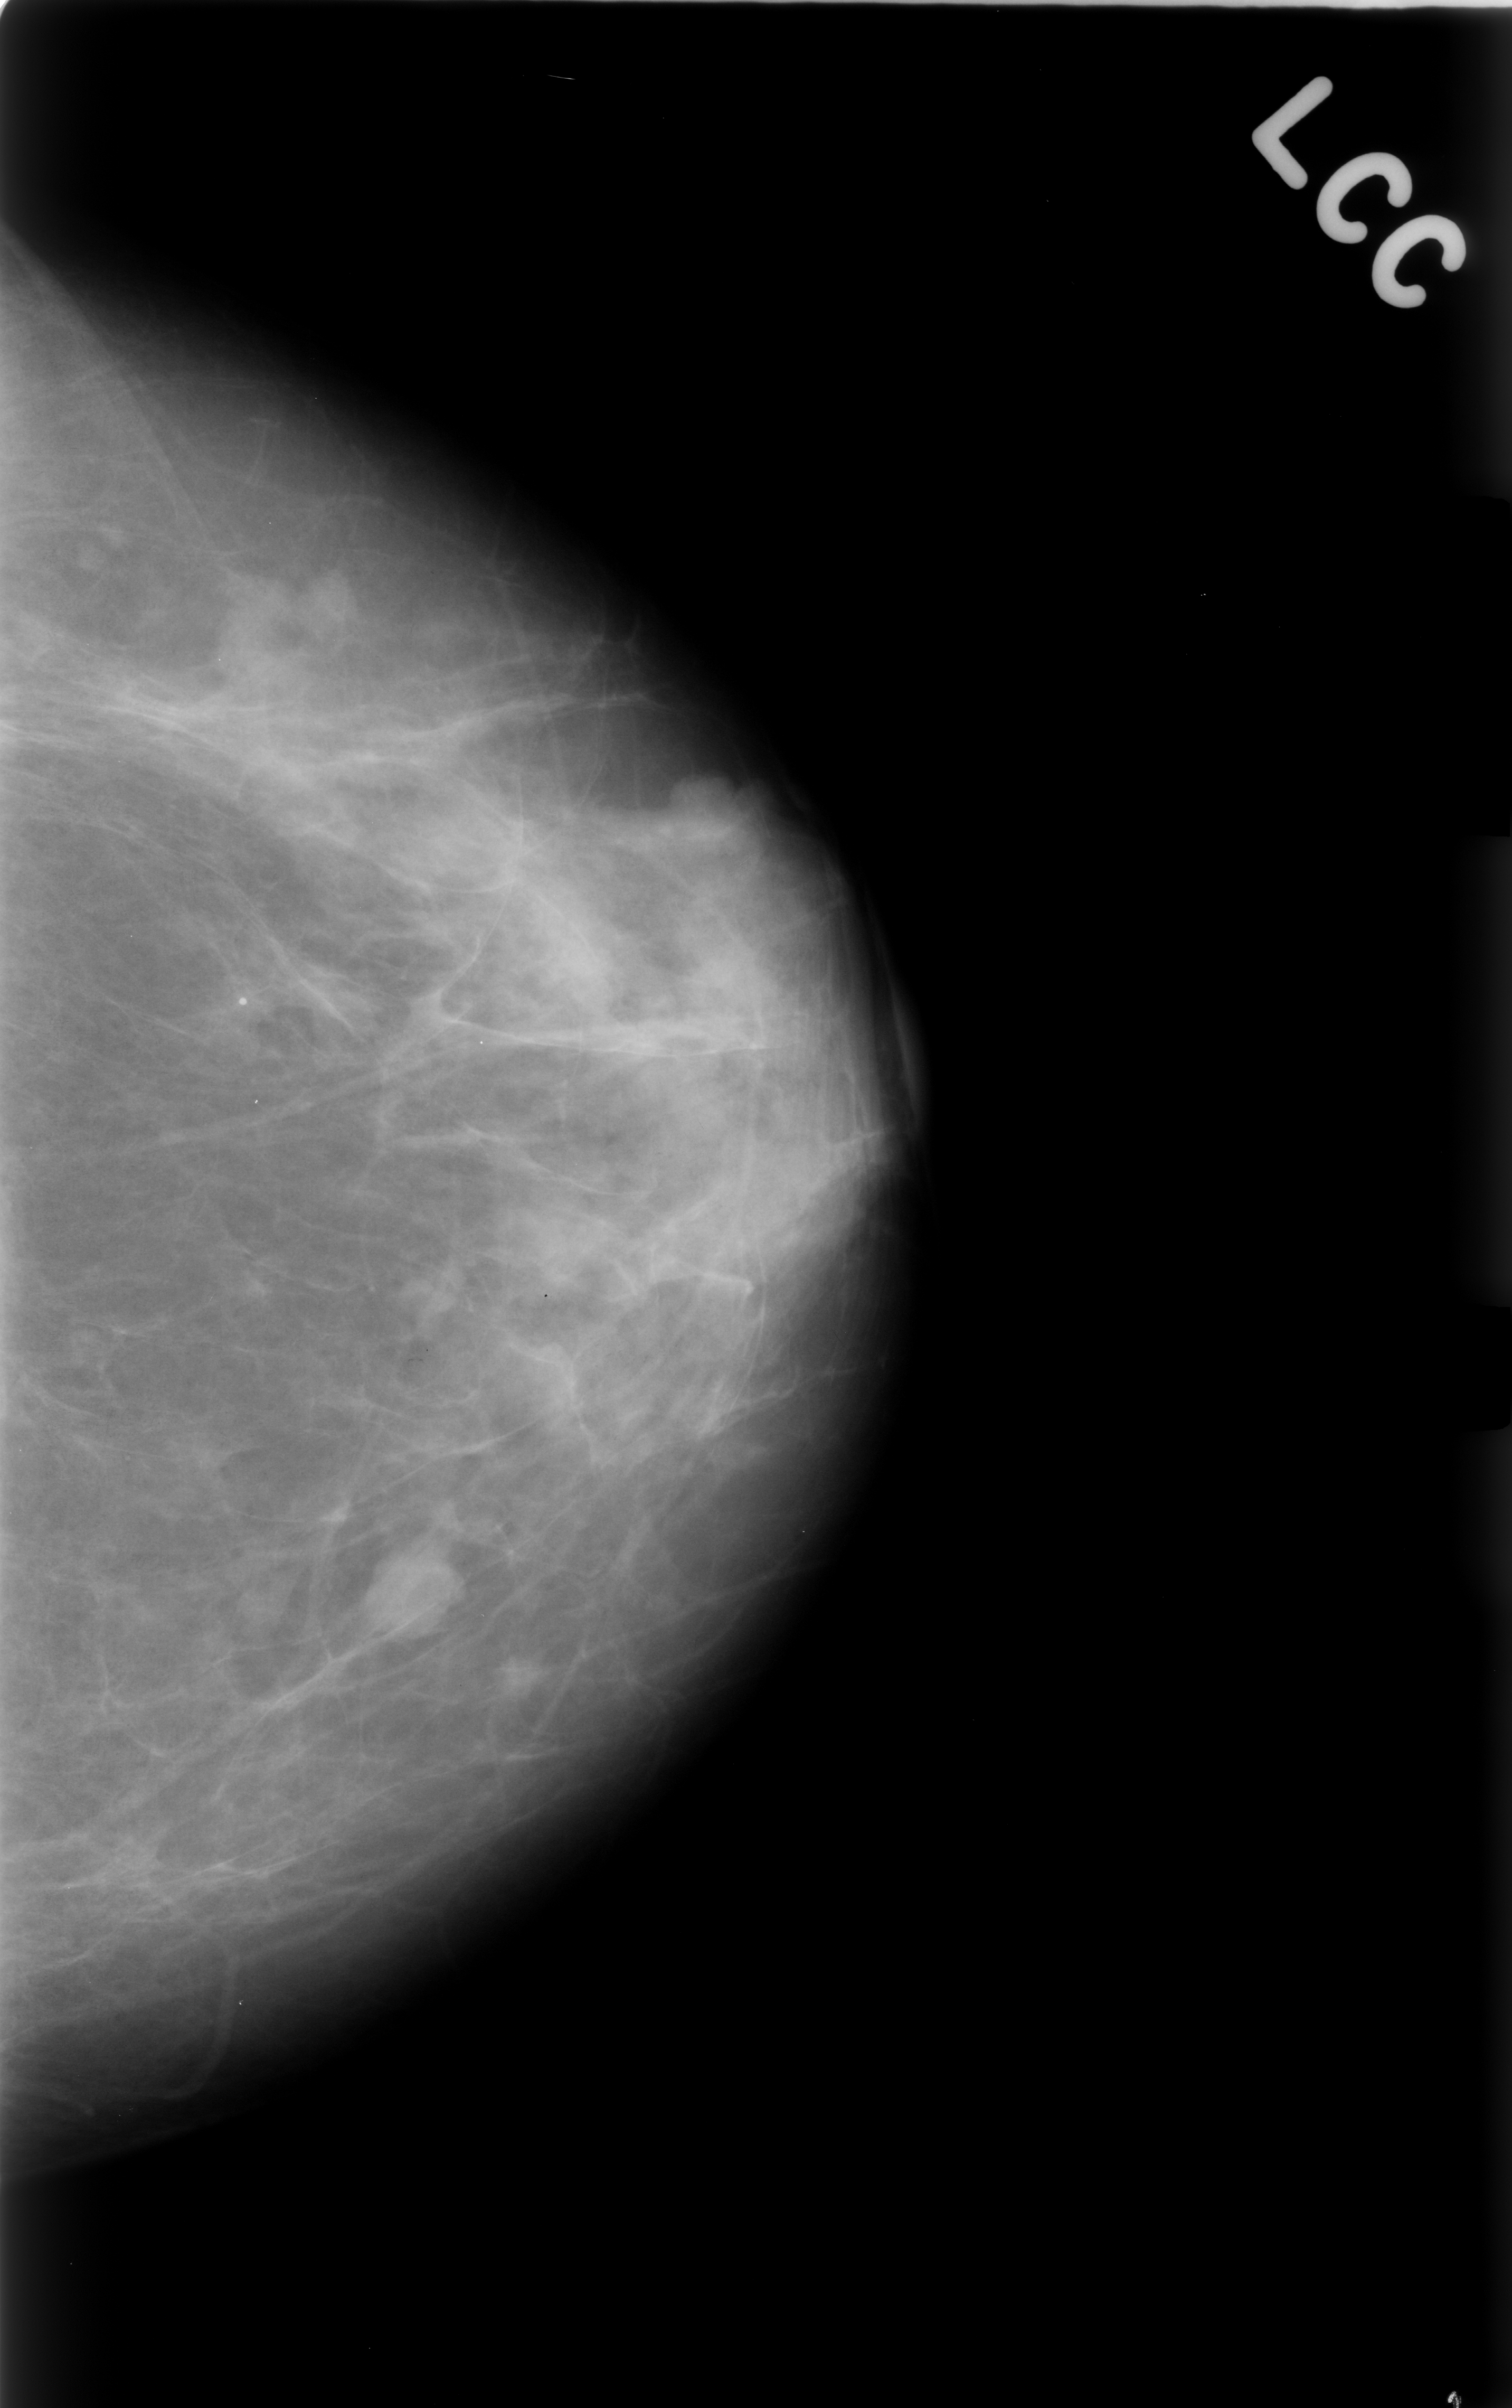
Digitized screen-film mammogram; left breast; CC view; breast composition: scattered fibroglandular densities (BI-RADS density category 2 of 4).
- Mass, shape lobulated, margins circumscribed; BI-RADS assessment category 4; pathology result (as recorded, not read from the image): benign.